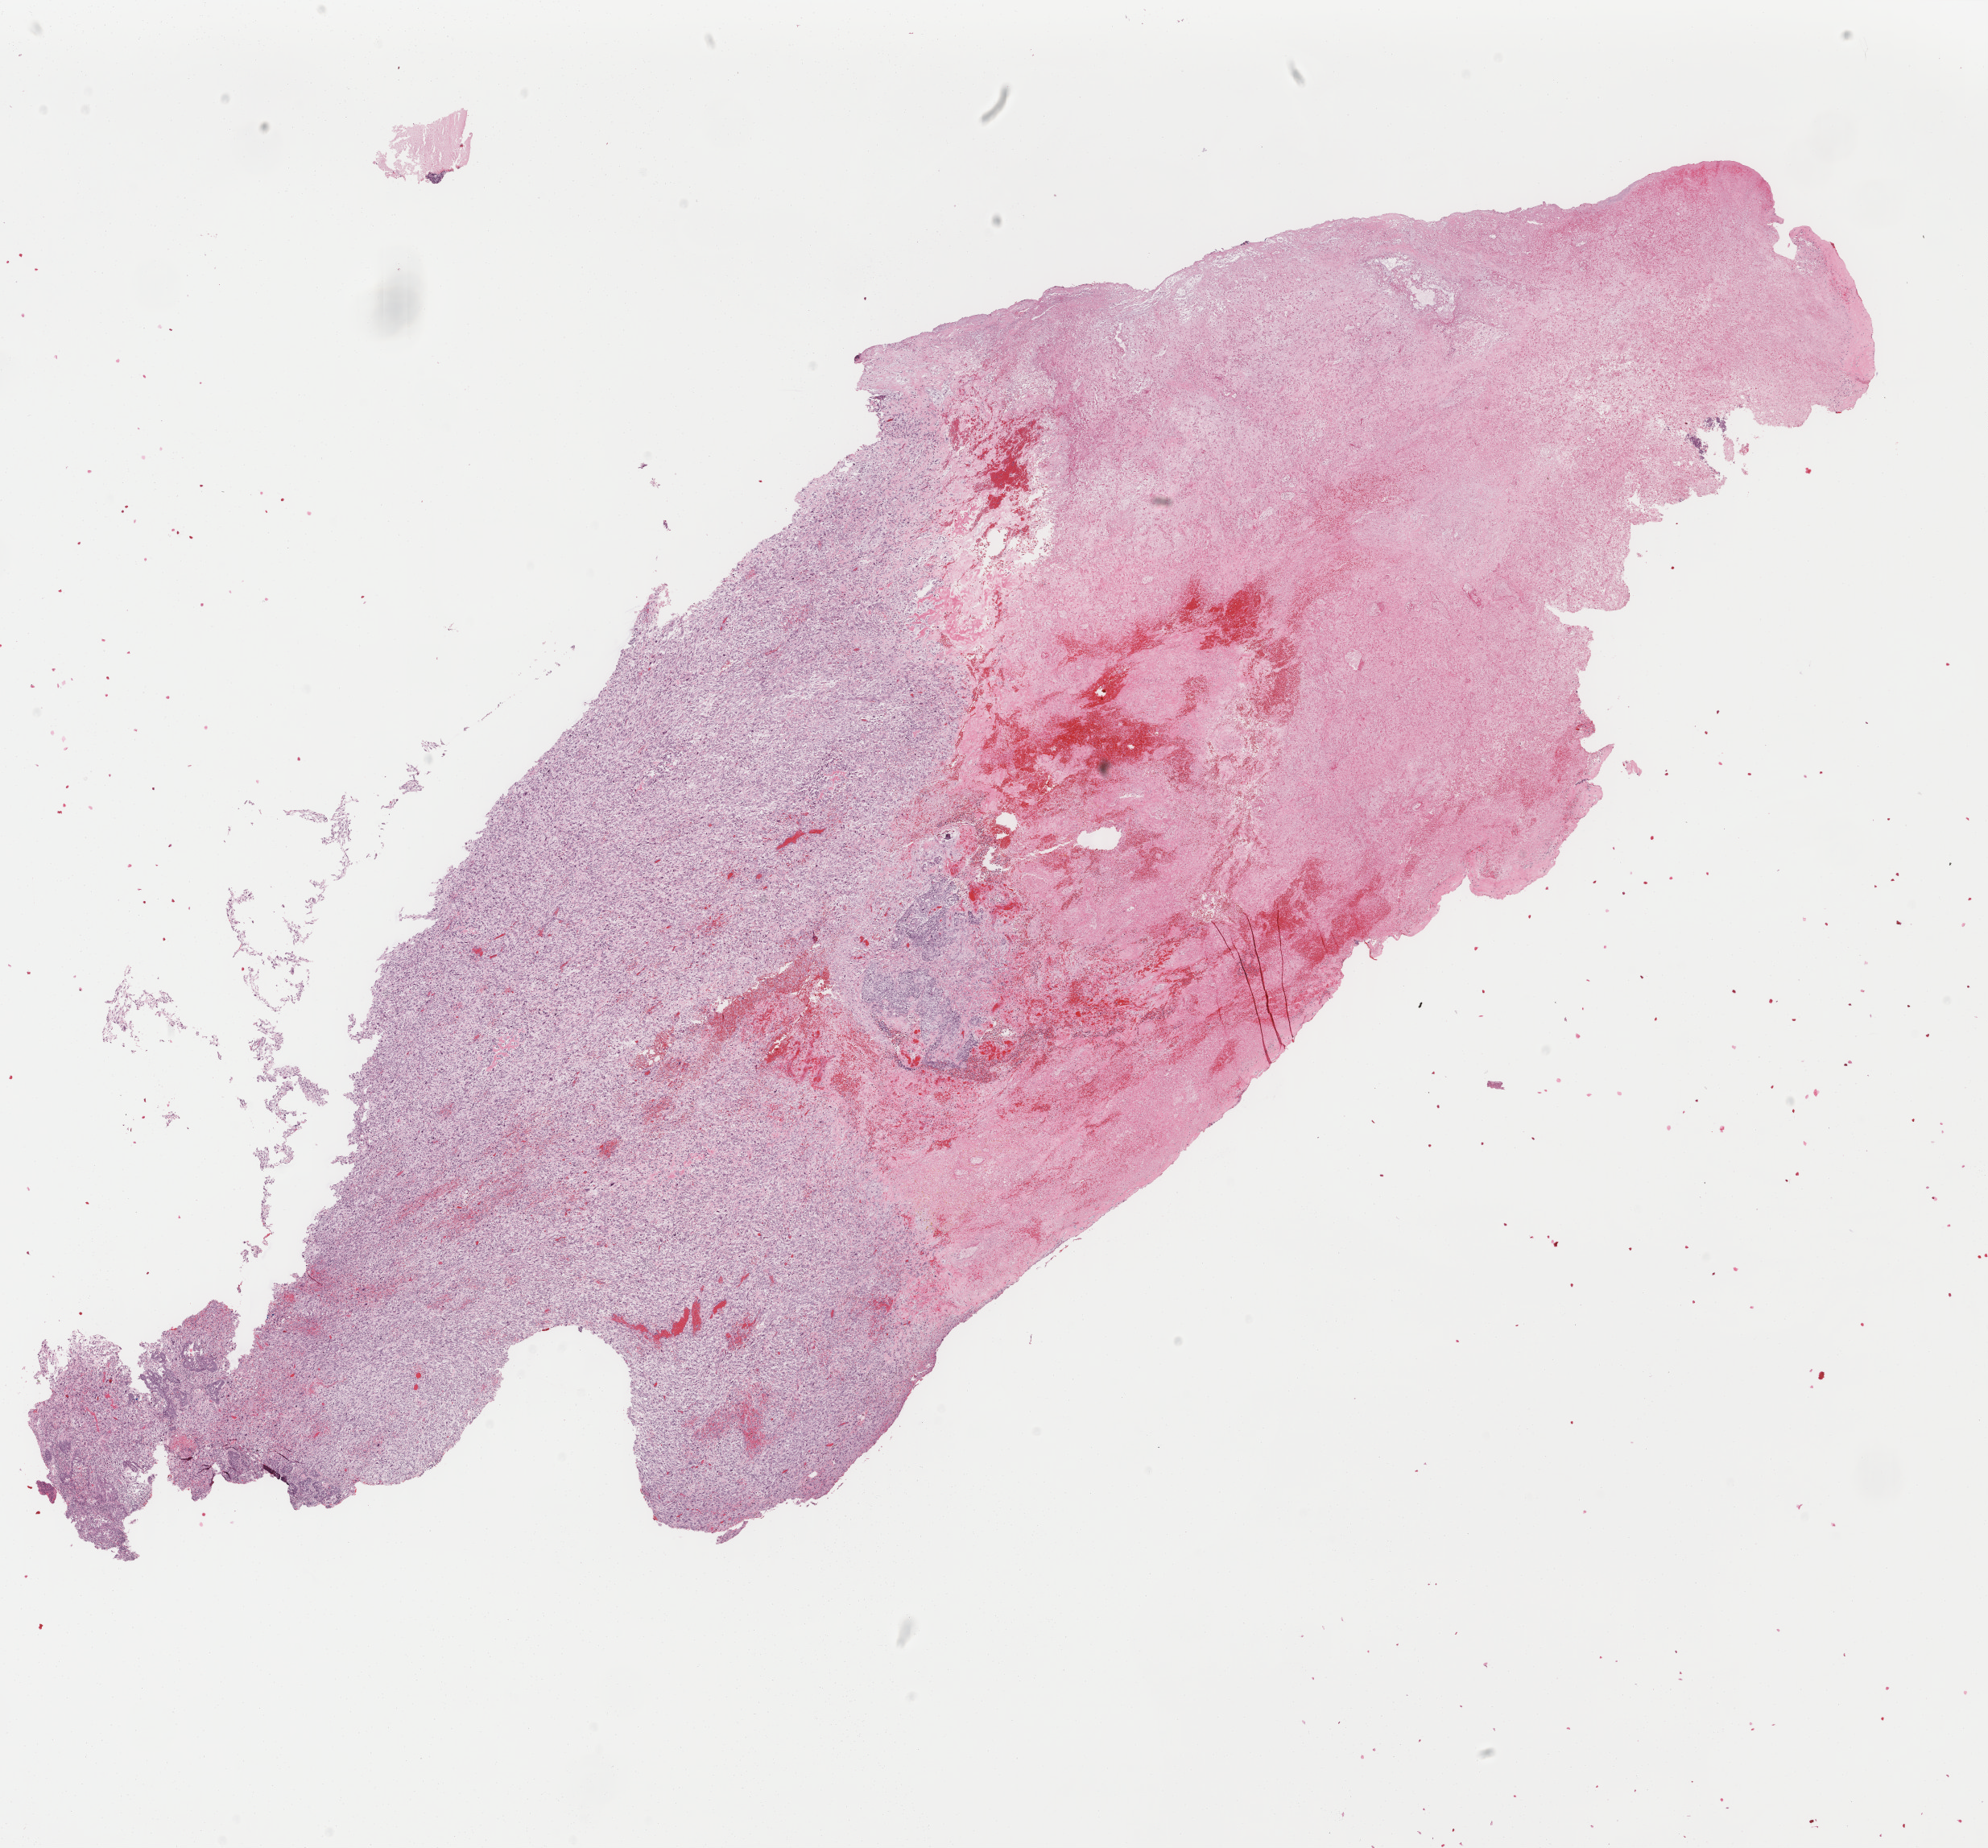
Hematoxylin and eosin (H&E) stained whole-slide image — shown as a low-resolution overview of the whole scanned area (about 19.6 x 18.2 mm, from a 40x scan). Formalin-fixed paraffin-embedded (FFPE) diagnostic section. Uterus, primary tumour sample. Patient: female, age at initial diagnosis 67 years.
FIGO stage: IA. Diagnosis: Mullerian mixed tumor (endometrium).